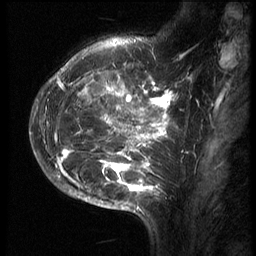
Breast MRI (dynamic contrast-enhanced), one sagittal slice; position 22 of 70 along the scan axis; 3 images stored at this slice position (order not interpretable as contrast timing); 1.5 T; TE 4.2 ms, TR 9 ms; 2.5 mm slice thickness; 256 × 256 image matrix, field of view 180 × 180 mm. Female patient, age 28 years. From the clinical record (not read from this slice): setting: breast cancer imaged before/during neoadjuvant chemotherapy.
Outlined on this slice (semi-automatic segmentation, software-assisted and operator-edited):
- analysis volume of interest (the breast-tissue region the enhancement analysis was run in; not a lesion): bounding box [x1, y1, x2, y2] px = [43, 42, 186, 215]
- tumour enhancement mask (voxels above the 140 % enhancement threshold inside the analysis volume of interest): [46, 53, 178, 209]